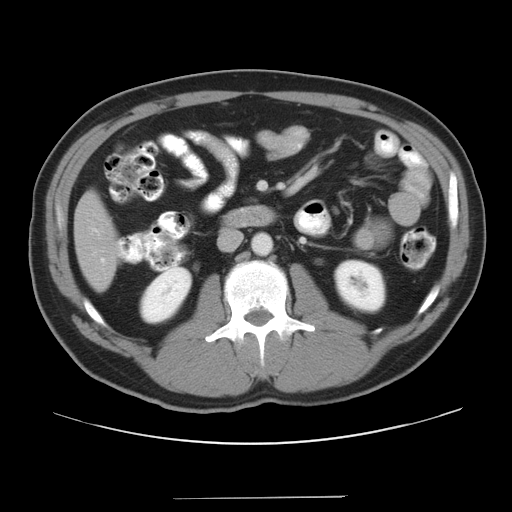
Contrast-enhanced abdominal CT, one axial slice. Slice 13 of 37 in the series (ordered by position). Soft-tissue window (W 400 / L 40 HU). 7.5 mm slice thickness. 512 × 512 image matrix. Male patient, age 46 years. Case-level facts recorded for this patient, not image findings: diagnosis: colorectal cancer liver metastases, imaged before liver resection; multiple liver metastases: yes; largest metastasis: 1 cm.
Outlined on this slice (outlined manually by an expert reader):
- hepatic veins: bounding box [x1, y1, x2, y2] px = [101, 258, 104, 262]
- liver: [76, 196, 117, 289]
- planned liver remnant (the part of the liver to remain after resection): [76, 196, 117, 290]